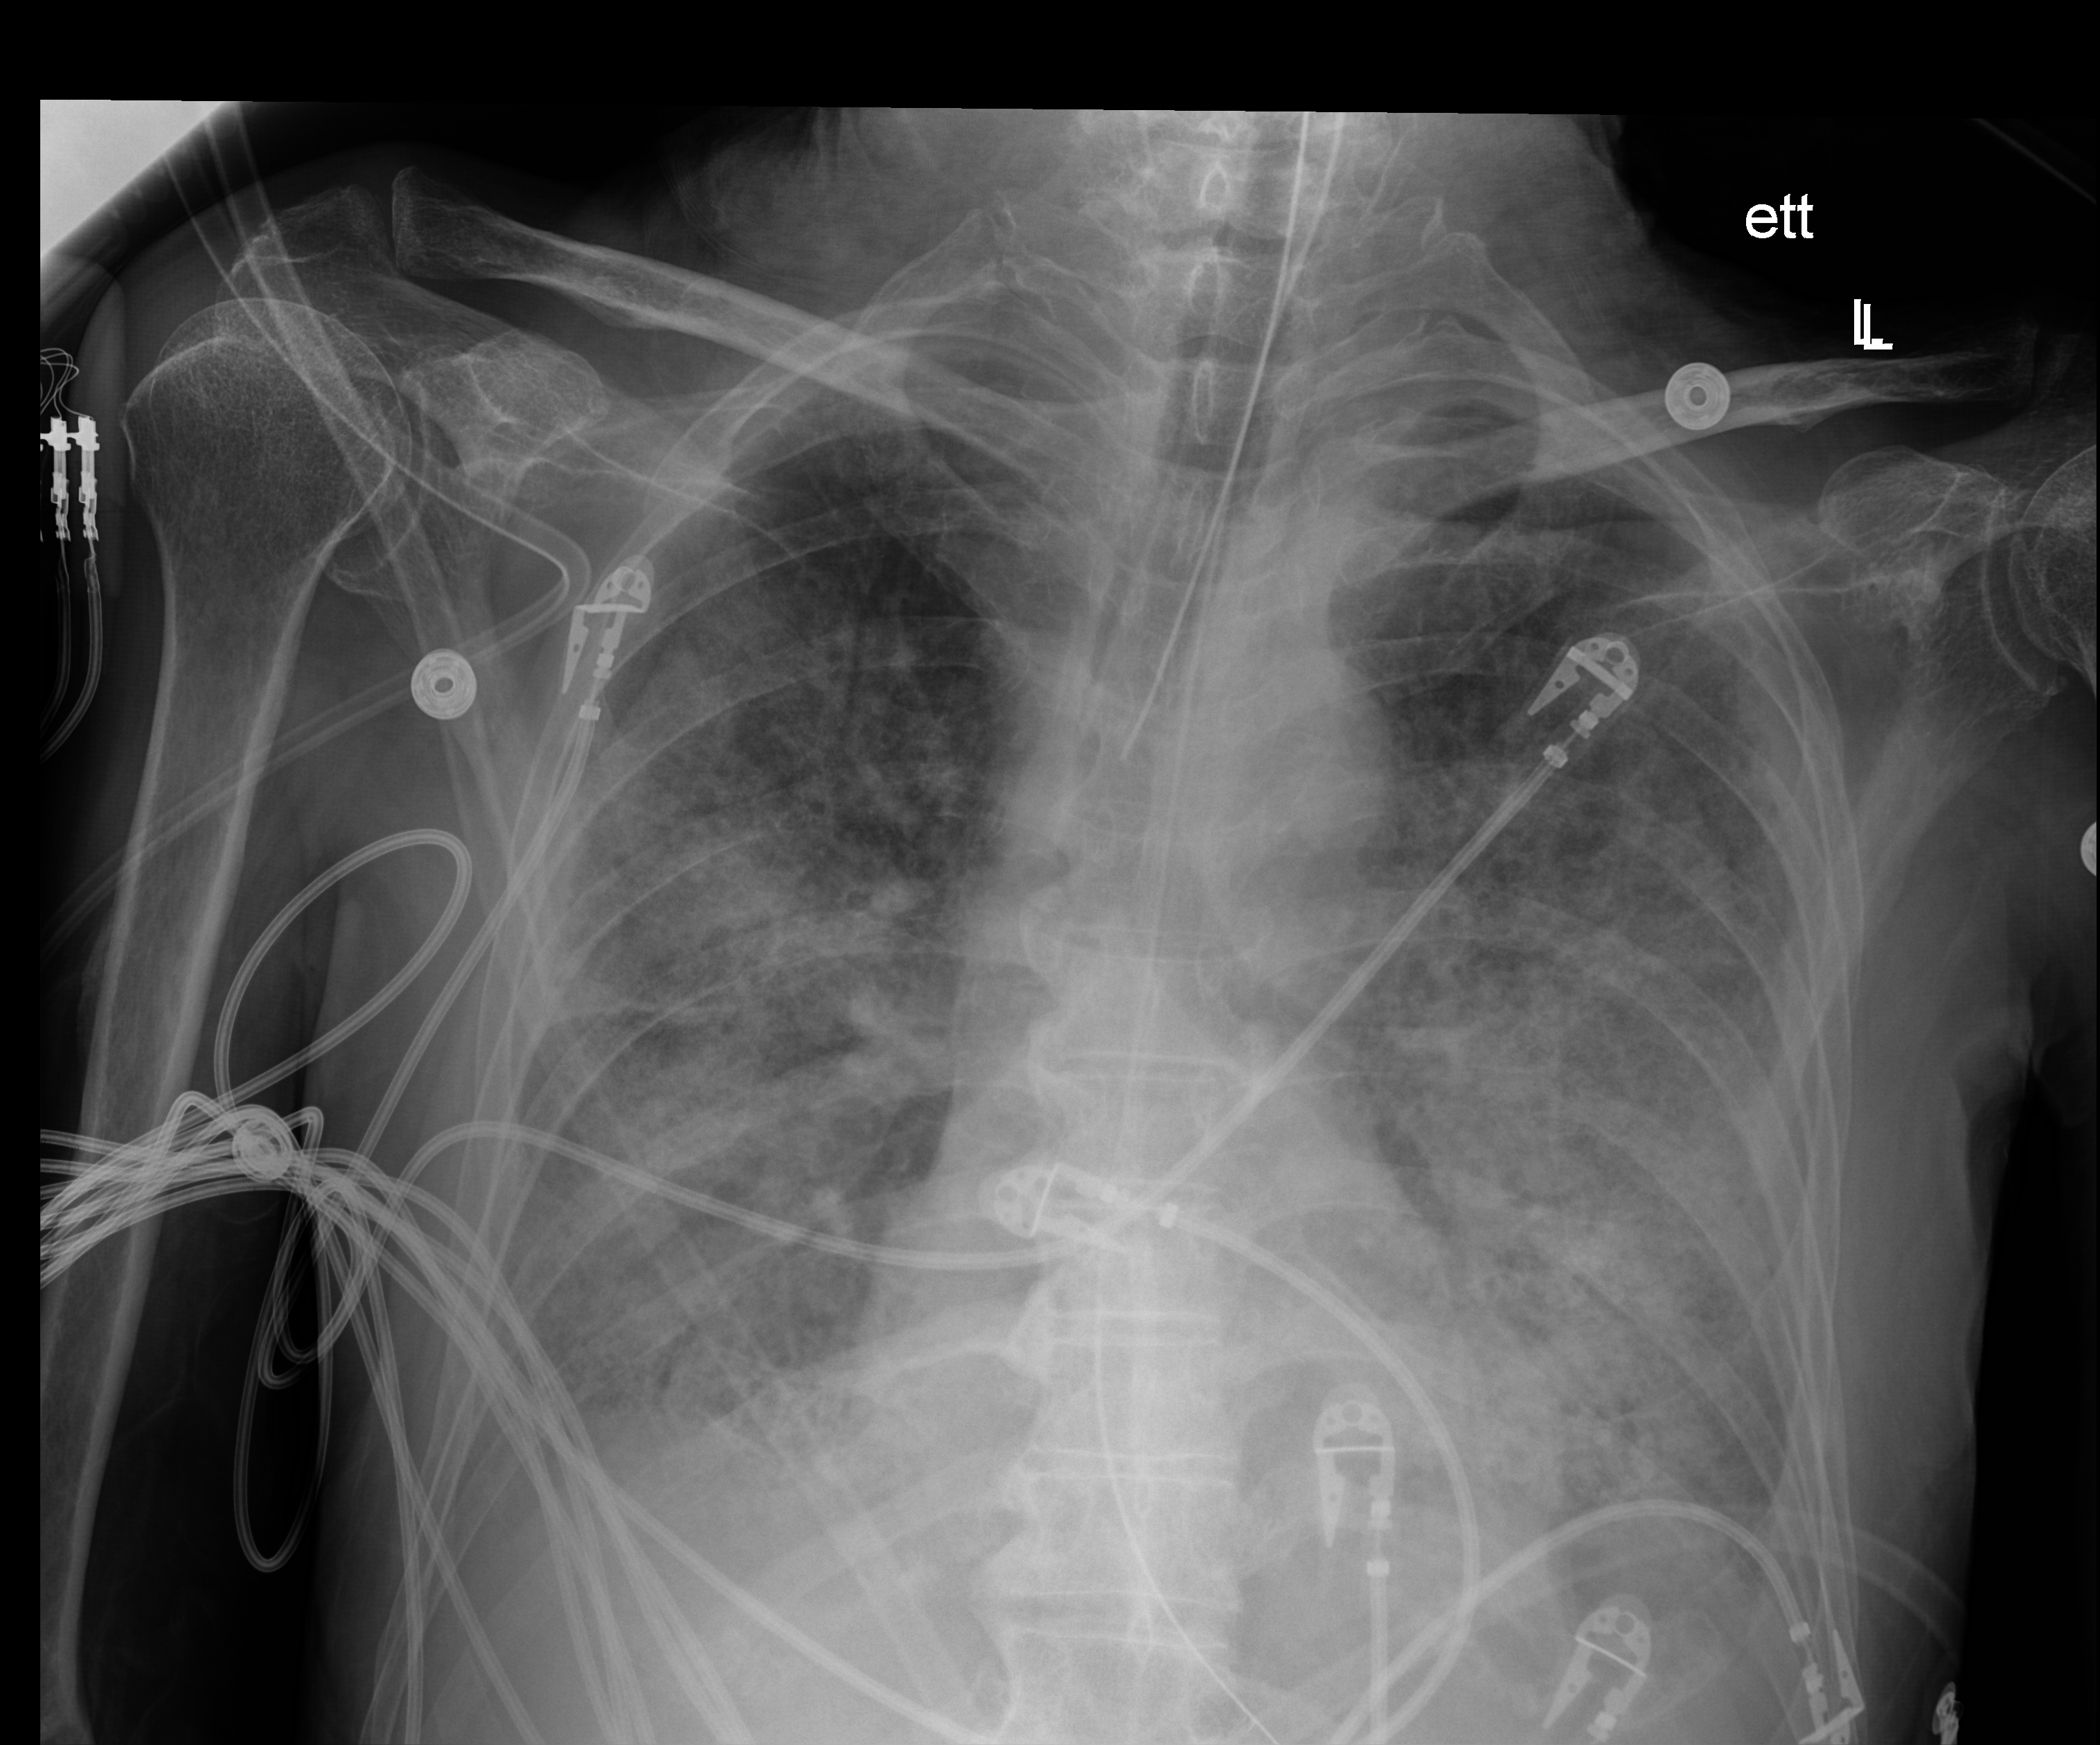
Chest X-ray (portable); anteroposterior (AP) projection. Patient hospitalised with COVID-19; male, aged 60–74 years.
Hospital-stay facts (about this admission, not read from this image; timing relative to this image not recorded):
- hypertension (admission record): yes